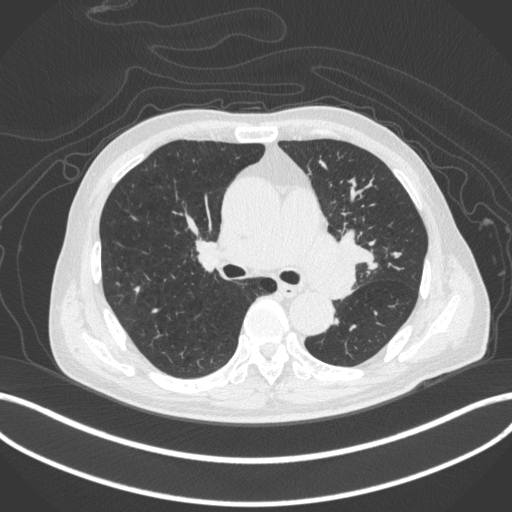
Chest CT, one axial slice; position 261 of 420 along the scan axis; reconstruction kernel B31f; 120 kVp; lung window (W 1500 / L -600 HU); 1 mm slice thickness; 512 × 512 image matrix, field of view 400 × 400 mm. Male patient, age 77 years. Case-level facts recorded for this patient, not image findings: clinical TNM (as recorded): T3 N1 M0.
Structures marked on this image (bounding box drawn by a radiologist):
- lung tumour (recorded histology: adenocarcinoma): bounding box <292,222,364,304> (left, top, right, bottom; pixels)